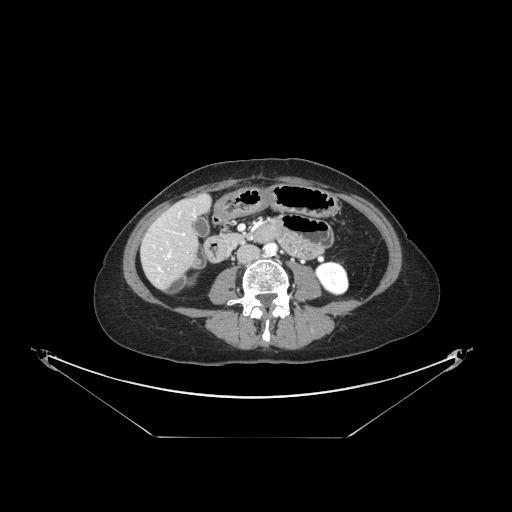
Contrast-enhanced abdominal CT, one axial slice; slice 40 of 148 in the series (ordered by position); reconstruction kernel STANDARD; 120 kVp; intravenous contrast given; soft-tissue window (W 400 / L 40 HU); 2.5 mm slice thickness; 512 × 512 image matrix. Female patient, age 73 years. Case-level facts recorded for this patient, not image findings: diagnosis: colorectal cancer liver metastases, imaged before liver resection; multiple liver metastases: no; largest metastasis: 1 cm; disease in both lobes: no.
Outlined on this slice (expert manual segmentation):
- hepatic veins: bounding box [x1, y1, x2, y2] px = [158, 234, 184, 271]
- liver: [143, 197, 210, 288]
- planned liver remnant (the part of the liver to remain after resection): [161, 197, 209, 241]